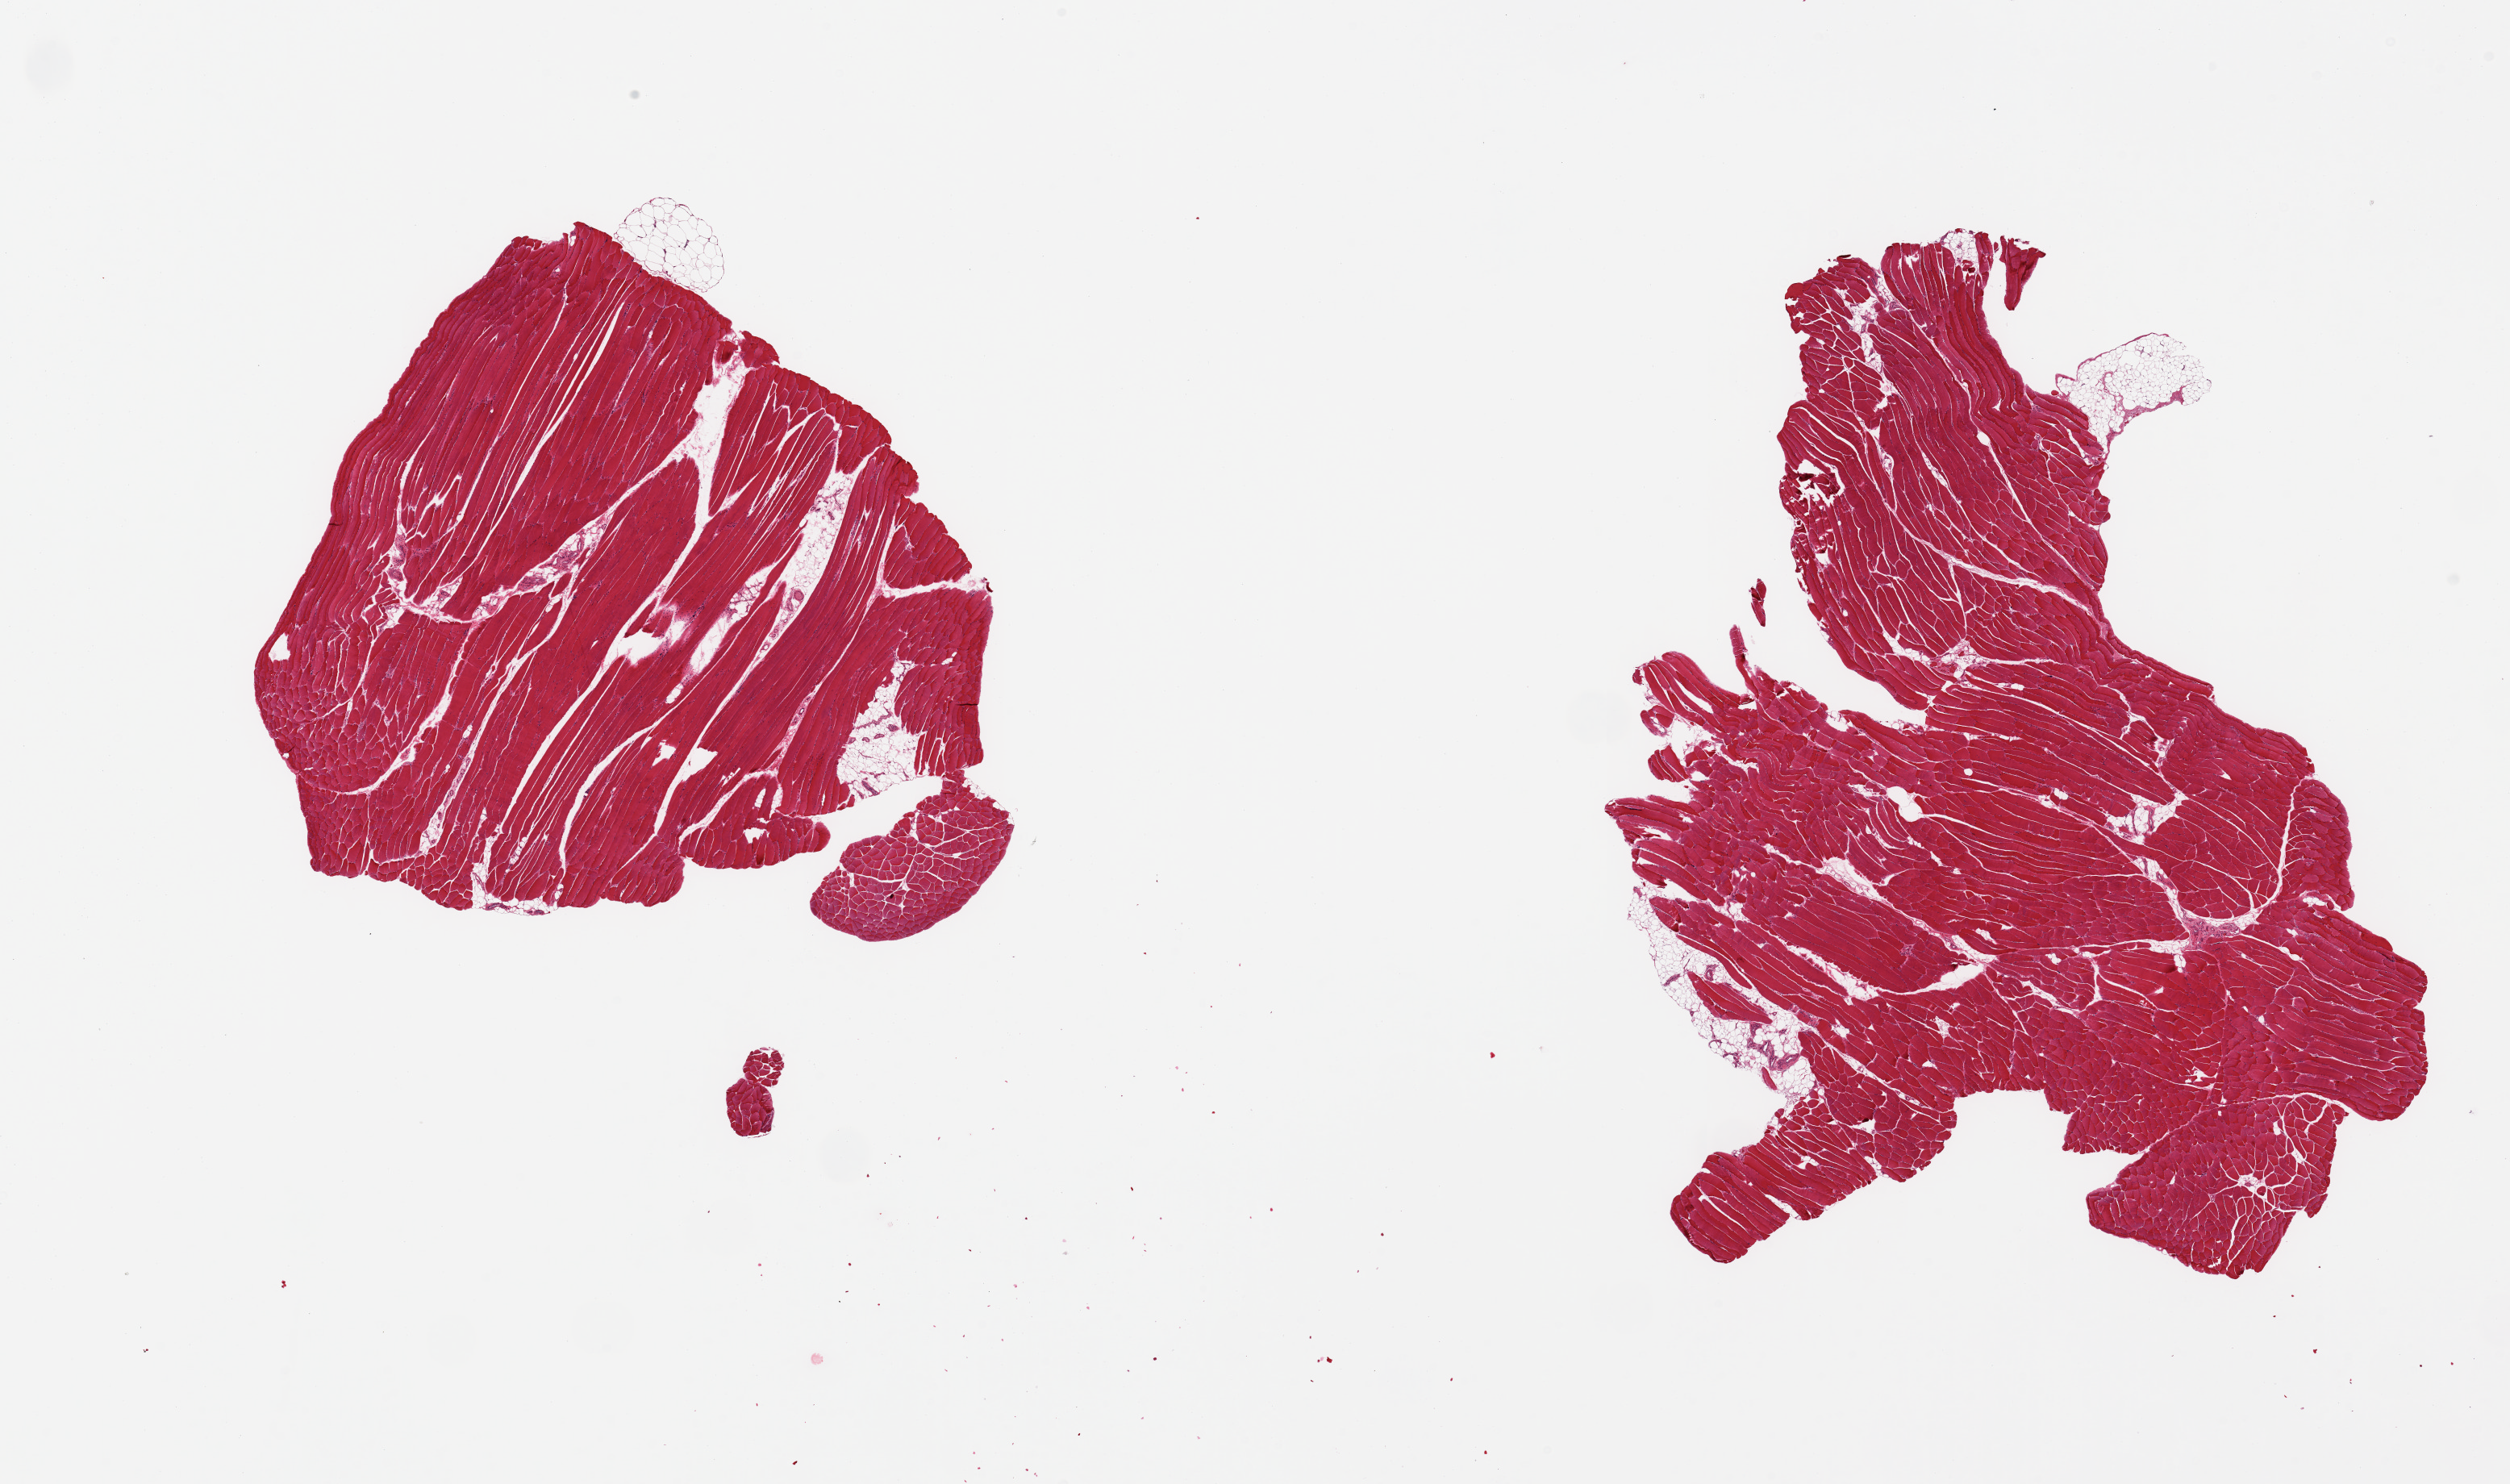
Whole-slide image, hematoxylin and eosin (H&E) stain, brightfield — low-resolution overview of the scanned area, about 24.6 x 14.6 mm. PAXgene-fixed, paraffin-embedded tissue. Target tissue: skeletal muscle. Donor tissue sample. Female donor.
Pathologist's review note for this sample: 2 pieces, ~10% interstitial fat.